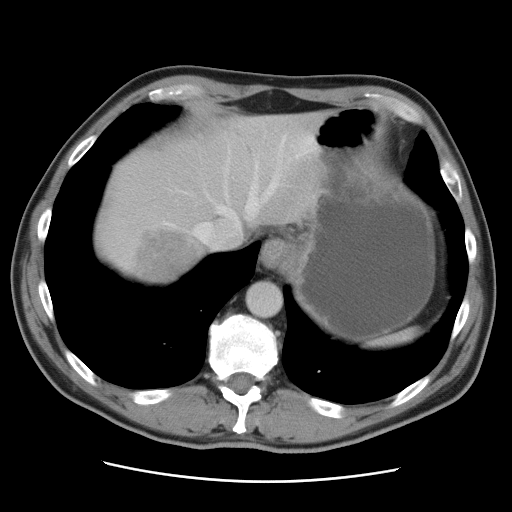
Contrast-enhanced abdominal CT, one axial slice. Position 77 of 89 along the scan axis. 120 kVp. Intravenous contrast given. Soft-tissue window (W 400 / L 40 HU). 512 × 512 image matrix, field of view 366 × 366 mm. Male patient, age 59 years. Case-level facts recorded for this patient, not image findings: diagnosis: colorectal cancer liver metastases, imaged before liver resection; multiple liver metastases: yes.
Structures marked on this image (outlined manually by an expert reader):
- hepatic veins: bounding box (x1, y1, x2, y2) in pixels: (181, 135, 287, 252)
- liver: (95, 112, 332, 286)
- planned liver remnant (the part of the liver to remain after resection): (134, 112, 333, 237)
- liver metastasis: (137, 232, 207, 284)